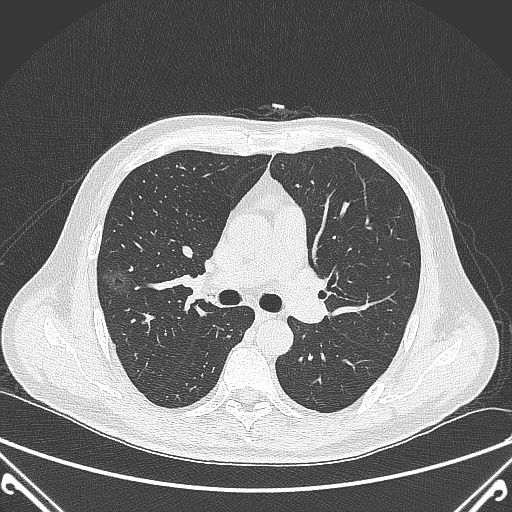
Chest CT, one axial slice. Position 226 of 360 along the scan axis. Lung window (W 1500 / L -600 HU). 1 mm slice thickness. 512 × 512 image matrix, field of view 380 × 380 mm. Male patient, age 64 years. Case-level facts recorded for this patient, not image findings: clinical TNM (as recorded): T1c N0 M0.
Structures marked on this image (bounding box drawn by a radiologist):
- lung tumour (recorded histology: adenocarcinoma): box from (x=107, y=265) to (x=134, y=303) px